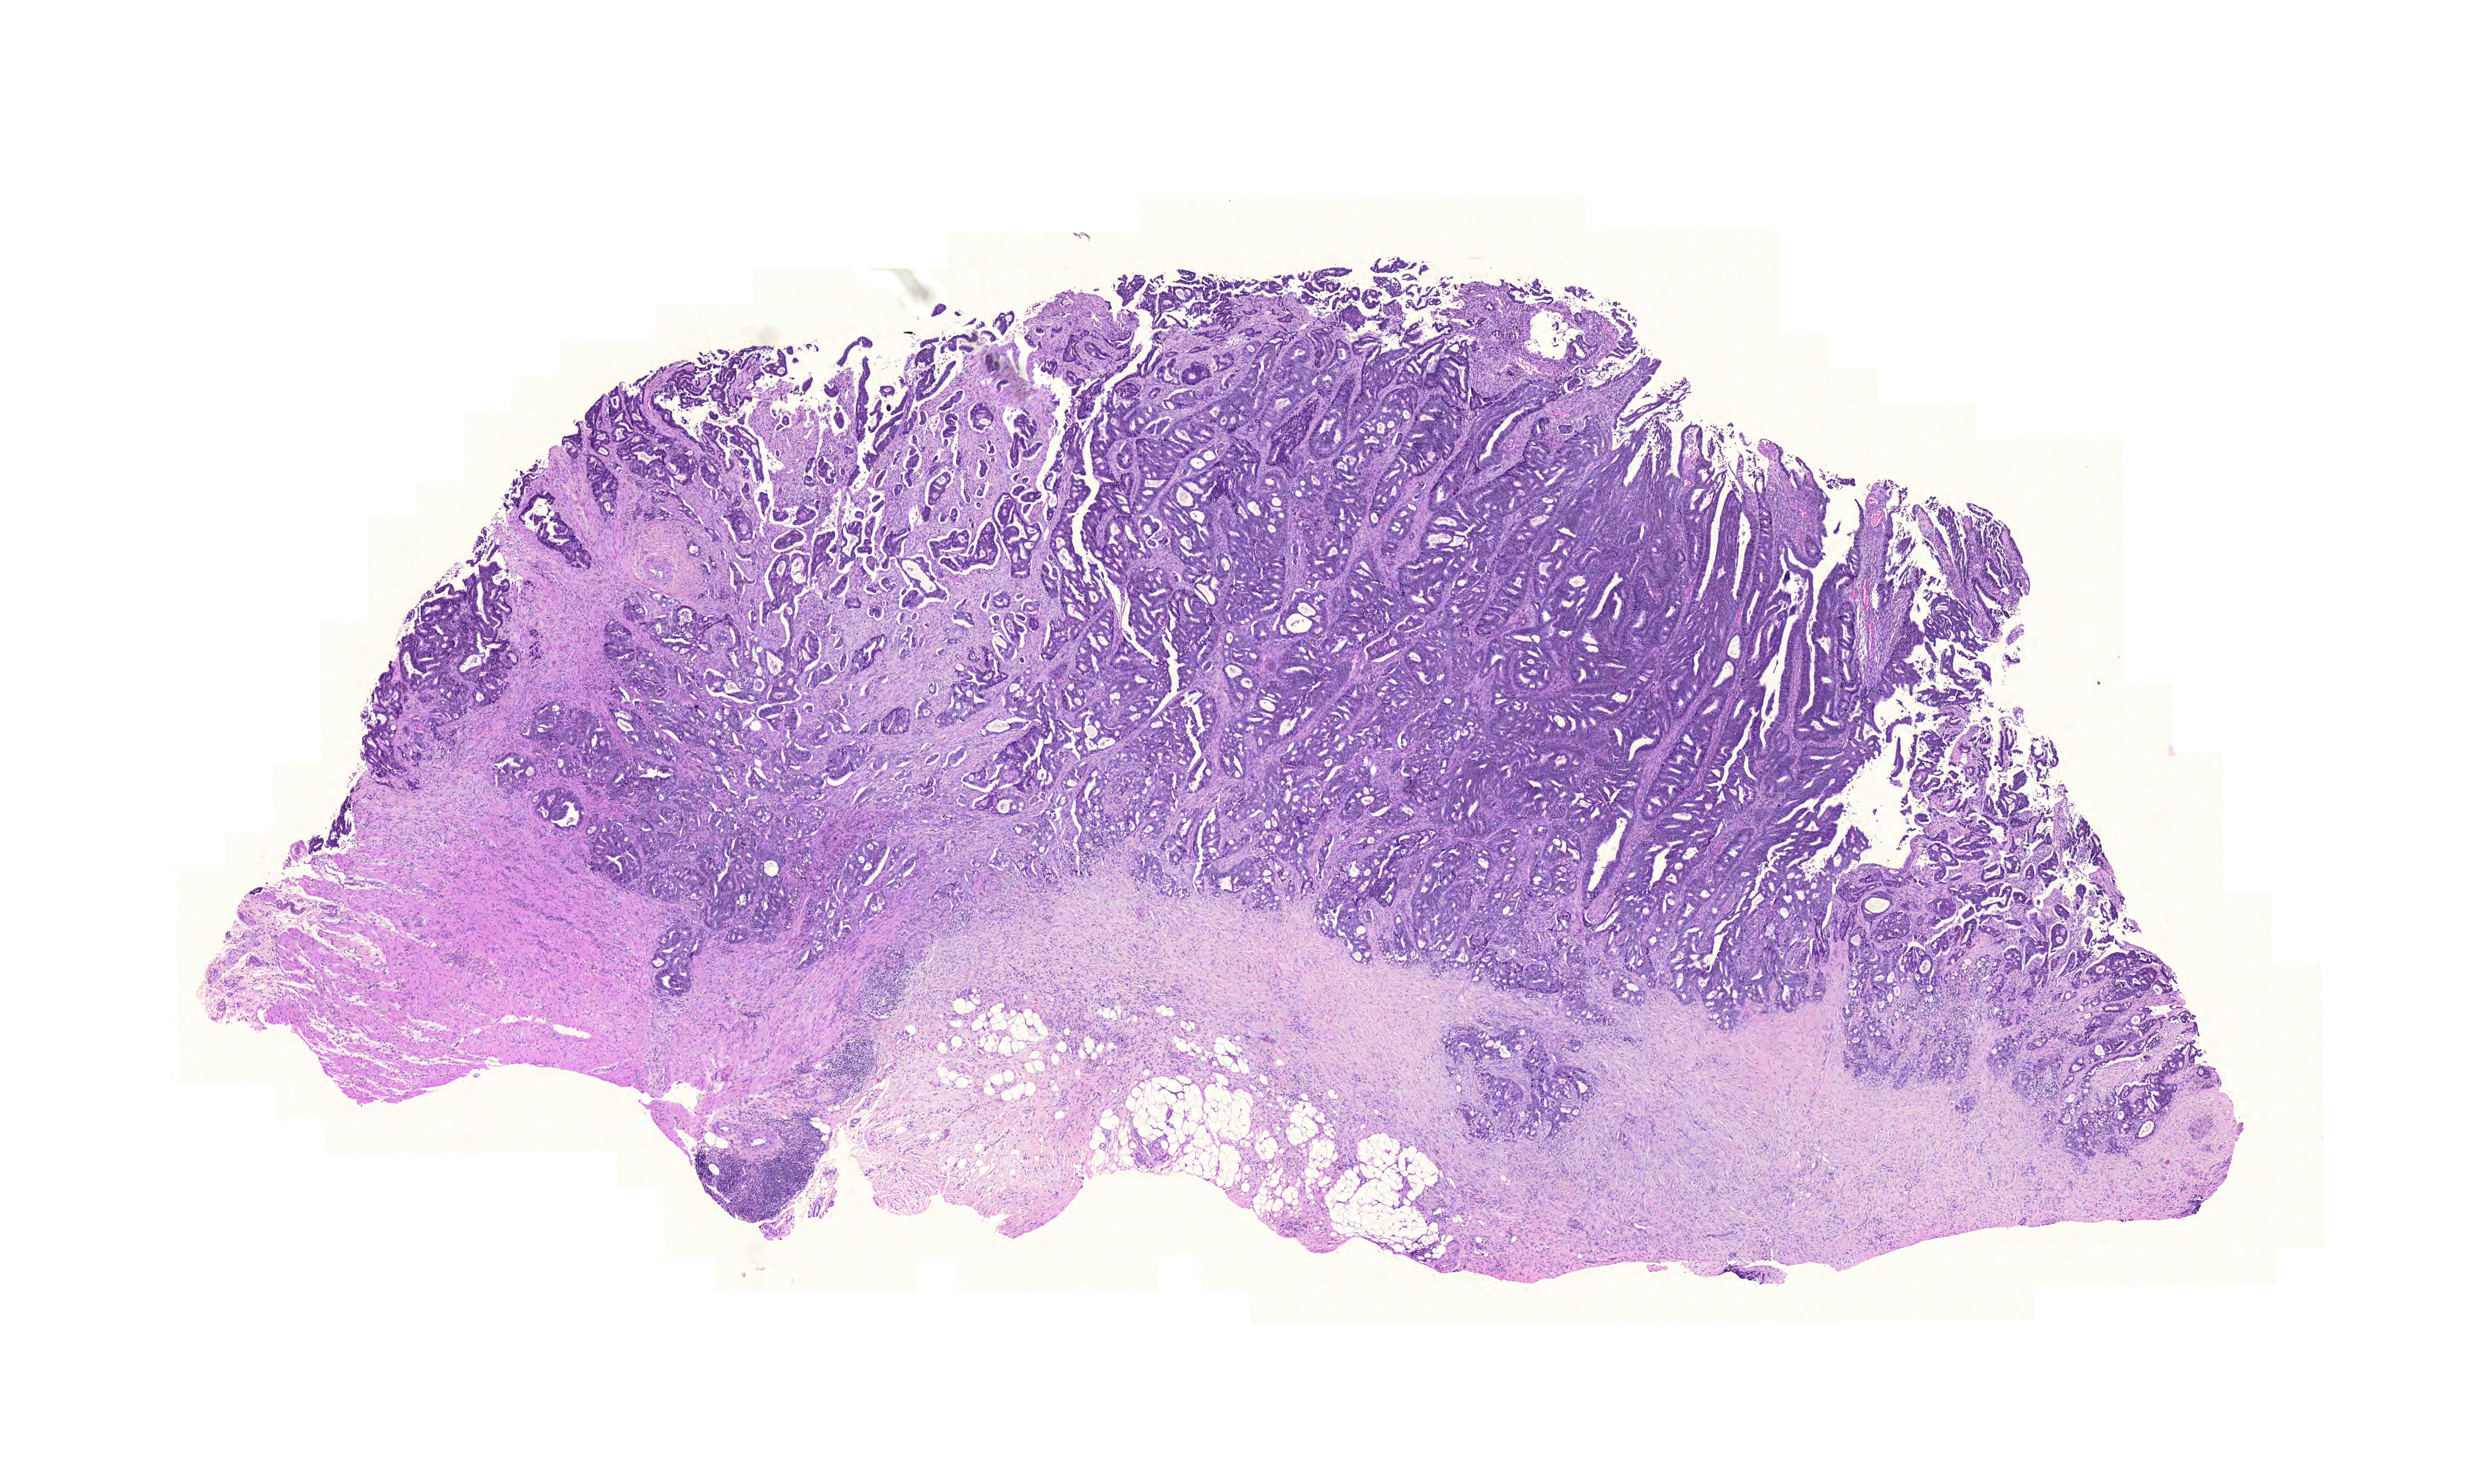
Digitized Hematoxylin and eosin (H&E) stained tissue section (whole slide) — low-resolution overview of the scanned area, about 14.6 x 8.7 mm (from a 20x scan). Formalin-fixed paraffin-embedded (FFPE) diagnostic section. Sample: primary tumour, colon. Male, age 69 years at initial diagnosis.
- AJCC pathologic stage: IV
- pathologic diagnosis: Adenocarcinoma, NOS
- lymph nodes positive (case pathology): 3 of 21 examined